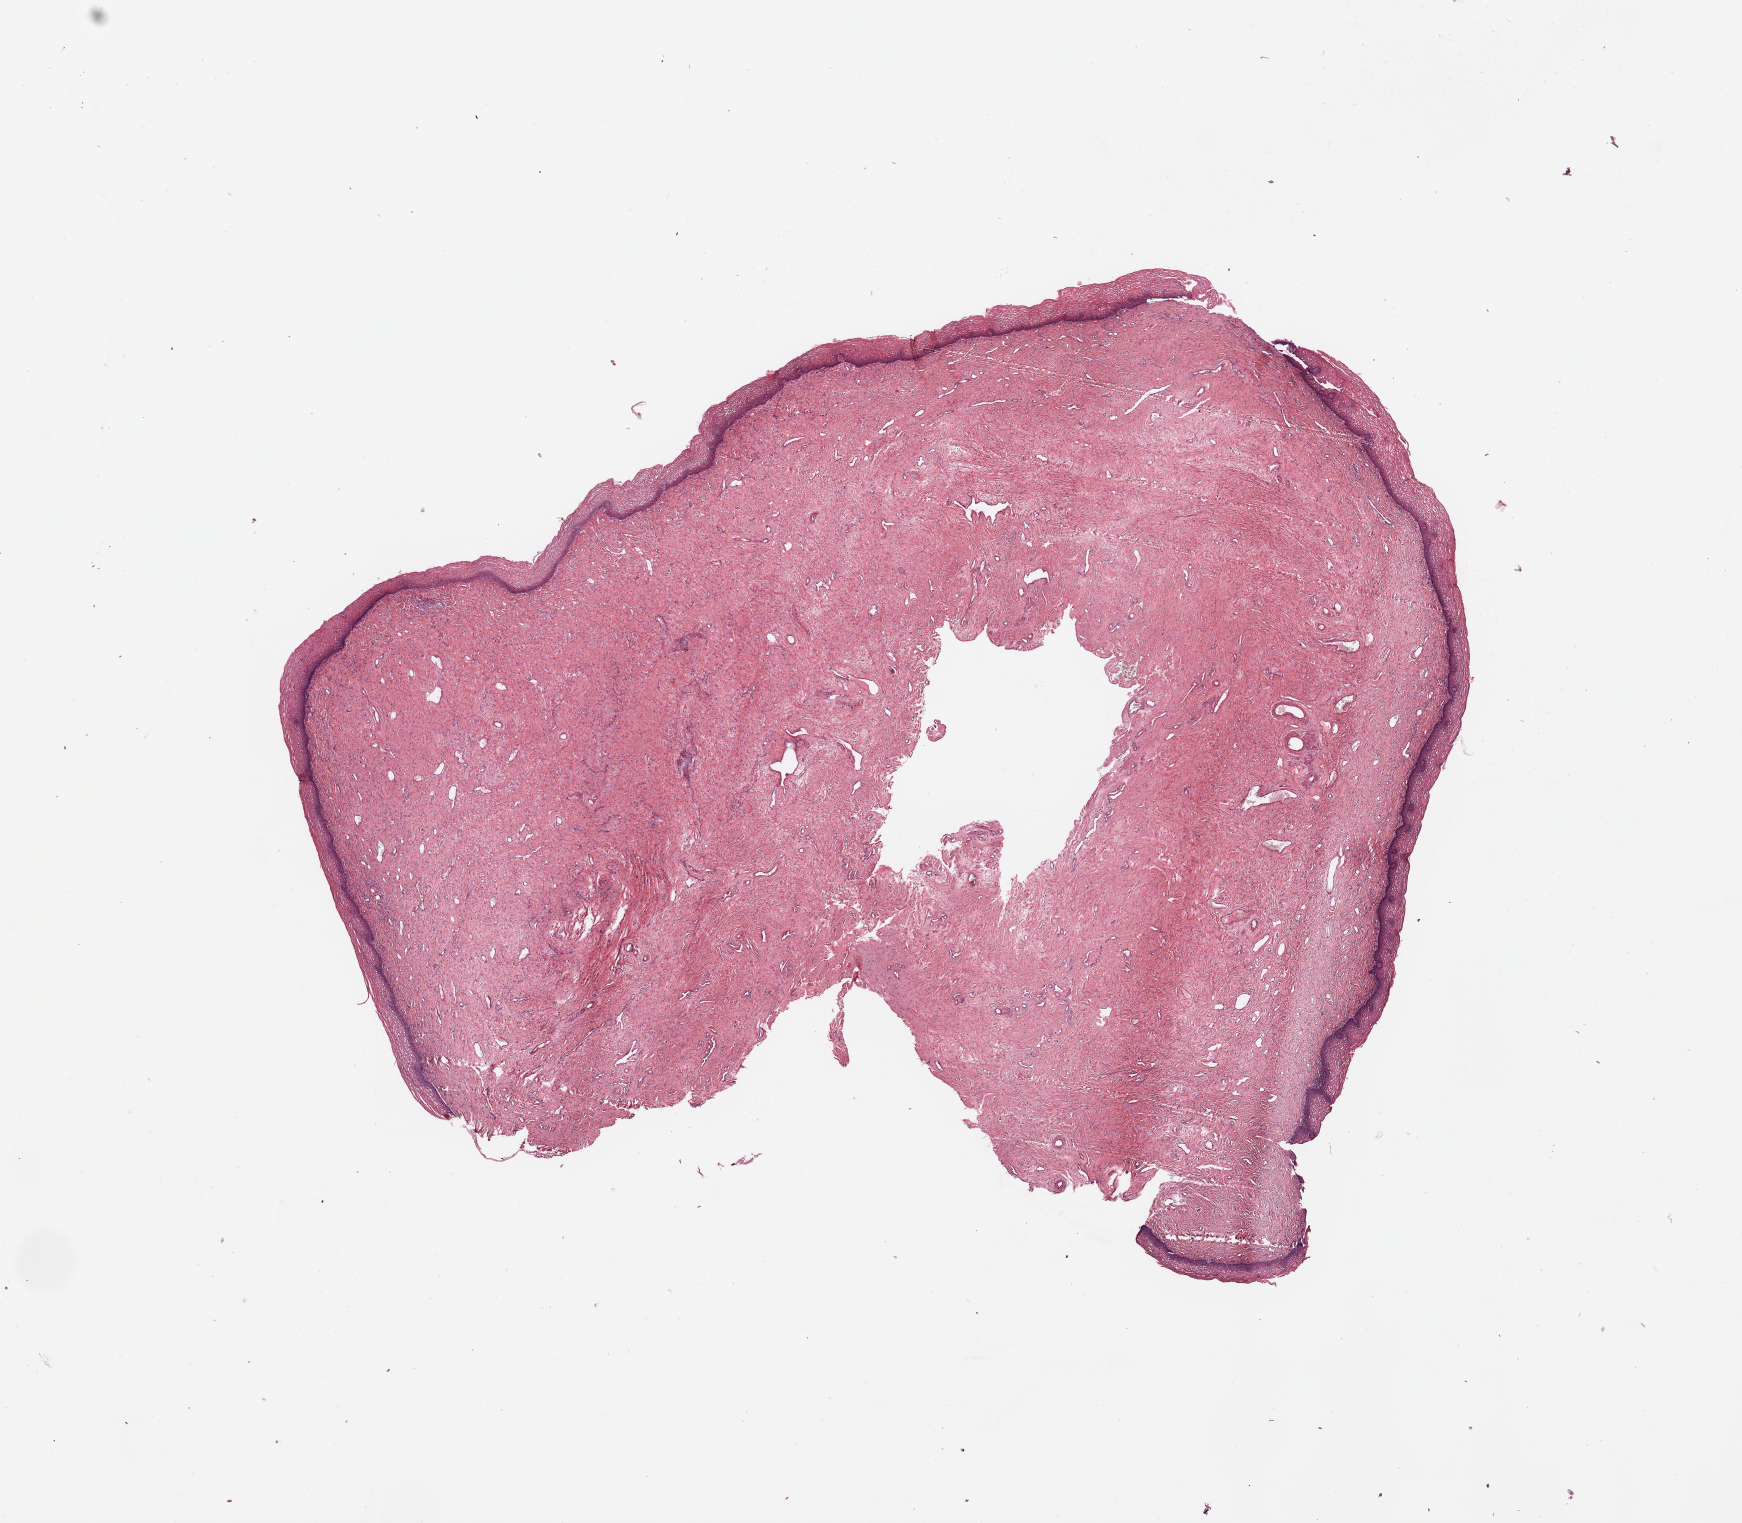
H&E whole-slide image, a low-resolution overview of the entire scanned area, about 13.8 x 12.0 mm. Normal (non-tumour) tissue sample, sampled site: uterus. Patient: female, age 57 years.
• this section: normal (non-tumour) tissue from the same patient
• patient diagnosis: Endometrioid adenocarcinoma, NOS